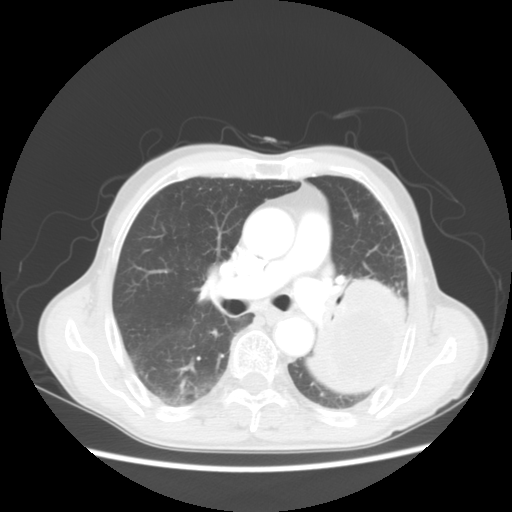
Chest CT, one axial slice; position 31 of 51 along the scan axis; reconstruction kernel STANDARD; 120 kVp; lung window (W 1500 / L -600 HU); 512 × 512 image matrix, field of view 360 × 360 mm. Patient: male, 64 years. Case-level facts recorded for this patient, not image findings: clinical TNM (as recorded): T4 N0 M0; histopathological grade: G2-3.
Annotated regions visible in this slice (bounding box drawn by a radiologist):
- lung tumour (recorded histology: squamous cell carcinoma): bounding box (x1, y1, x2, y2) in pixels: (315, 262, 416, 393)